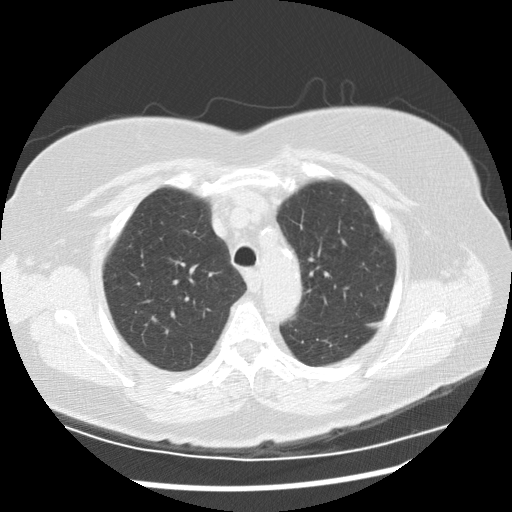
Chest CT (low-dose screening protocol), one axial image, second screening round (one year after baseline), lung window (W 1500 / L -600 HU). Female participant, aged 72 years at enrolment. Current smoker at enrolment.
Lesion marked by an expert reader, box from (x=139, y=310) to (x=166, y=333) px. Screening reader's record for this exam: no non-calcified nodule ≥4 mm recorded. Official screen result: negative screen, minor abnormalities not suspicious for lung cancer. Lung cancer was diagnosed 507 days after this screen (after the third annual screen): squamous cell carcinoma, NOS, right upper lobe, poorly differentiated (G3), stage IIIA (AJCC 6th edition), 22 mm at pathology.